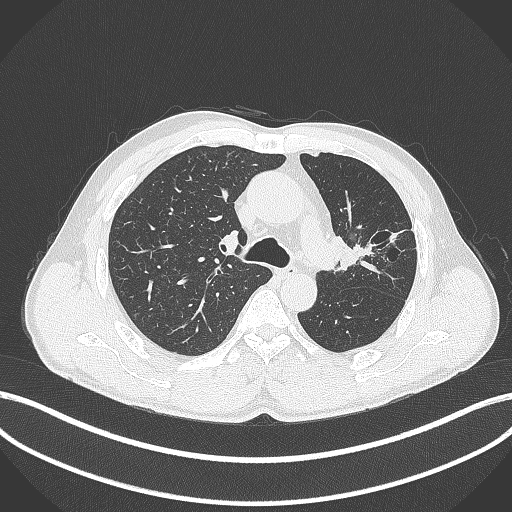
Chest CT, one axial slice; position 280 of 429 along the scan axis; reconstruction kernel B70f; 120 kVp; lung window (W 1500 / L -600 HU); 512 × 512 image matrix. Patient: male, 57 years. From the clinical record (not read from this slice): clinical TNM (as recorded): T2b N0 M0.
Outlined on this slice (rectangle marked by the reading radiologist):
- lung tumour (recorded histology: squamous cell carcinoma): box from (x=332, y=230) to (x=383, y=281) px